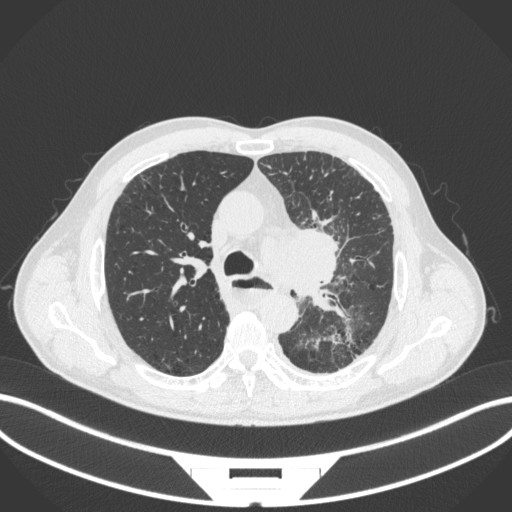
Chest CT, one axial slice. Slice 260 of 411 in the series (ordered by position). Reconstruction kernel B31f. 120 kVp. Lung window (W 1500 / L -600 HU). 512 × 512 image matrix, field of view 400 × 400 mm. Patient: male, 57 years. Case-level facts recorded for this patient, not image findings: clinical TNM (as recorded): T2a N1 M0.
Outlined on this slice (bounding box drawn by a radiologist):
- lung tumour (recorded histology: squamous cell carcinoma): box from (x=256, y=214) to (x=345, y=296) px